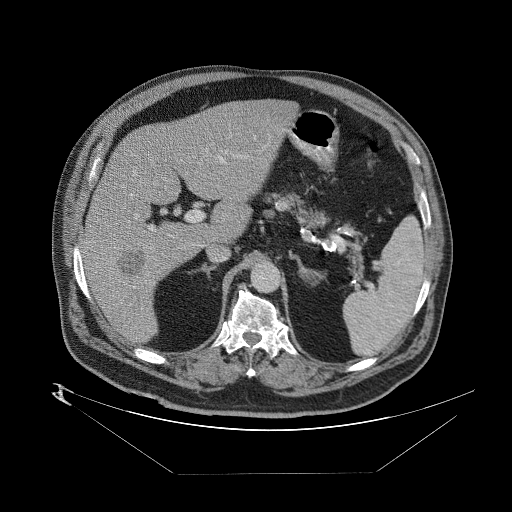
Contrast-enhanced abdominal CT (liver protocol), one axial slice. Position 46 of 89 along the scan axis. Reconstruction kernel STANDARD. 140 kVp. One of 2 acquisitions stored at this slice position. Soft-tissue window (W 400 / L 40 HU). 2.5 mm slice thickness. 512 × 512 image matrix, field of view 480 × 480 mm. From the clinical record (not read from this slice): diagnosis: hepatocellular carcinoma (patient treated with transarterial chemoembolisation; whether this scan precedes or follows treatment is not stated here); TNM stage (as recorded): Stage-II; Child-Pugh class: B; tumour nodularity: multinodular; tumour size: 4 cm.
Structures marked on this image (semi-automatic segmentation, software-assisted and operator-edited):
- abdominal aorta: bounding box <251,262,280,291> (left, top, right, bottom; pixels)
- liver parenchyma outside the tumour (the mass and vessels are separate outlines, so this box may not span the whole liver): <82,96,292,344>
- mass: <114,246,155,280>
- liver vessels: <88,120,284,290>